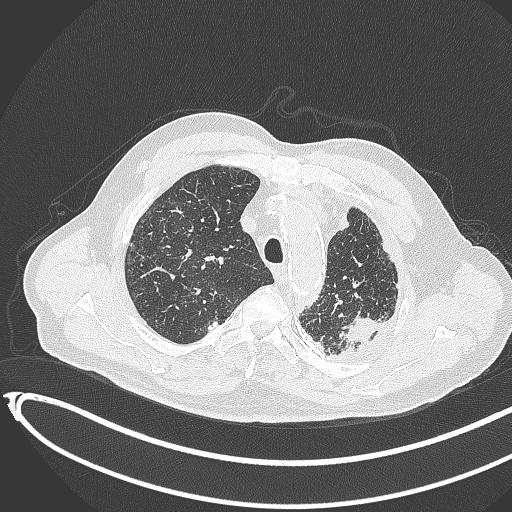
Chest CT, one axial slice. Slice 342 of 451 in the series (ordered by position). Reconstruction kernel B70f. 120 kVp. Lung window (W 1500 / L -600 HU). 1 mm slice thickness. 512 × 512 image matrix, field of view 400 × 400 mm. Male patient, age 78 years. Case-level facts recorded for this patient, not image findings: clinical TNM (as recorded): T1c N0 M1.
Annotated regions visible in this slice (bounding box drawn by a radiologist):
- lung tumour (recorded histology: adenocarcinoma): bounding box [x1, y1, x2, y2] px = [342, 310, 383, 346]